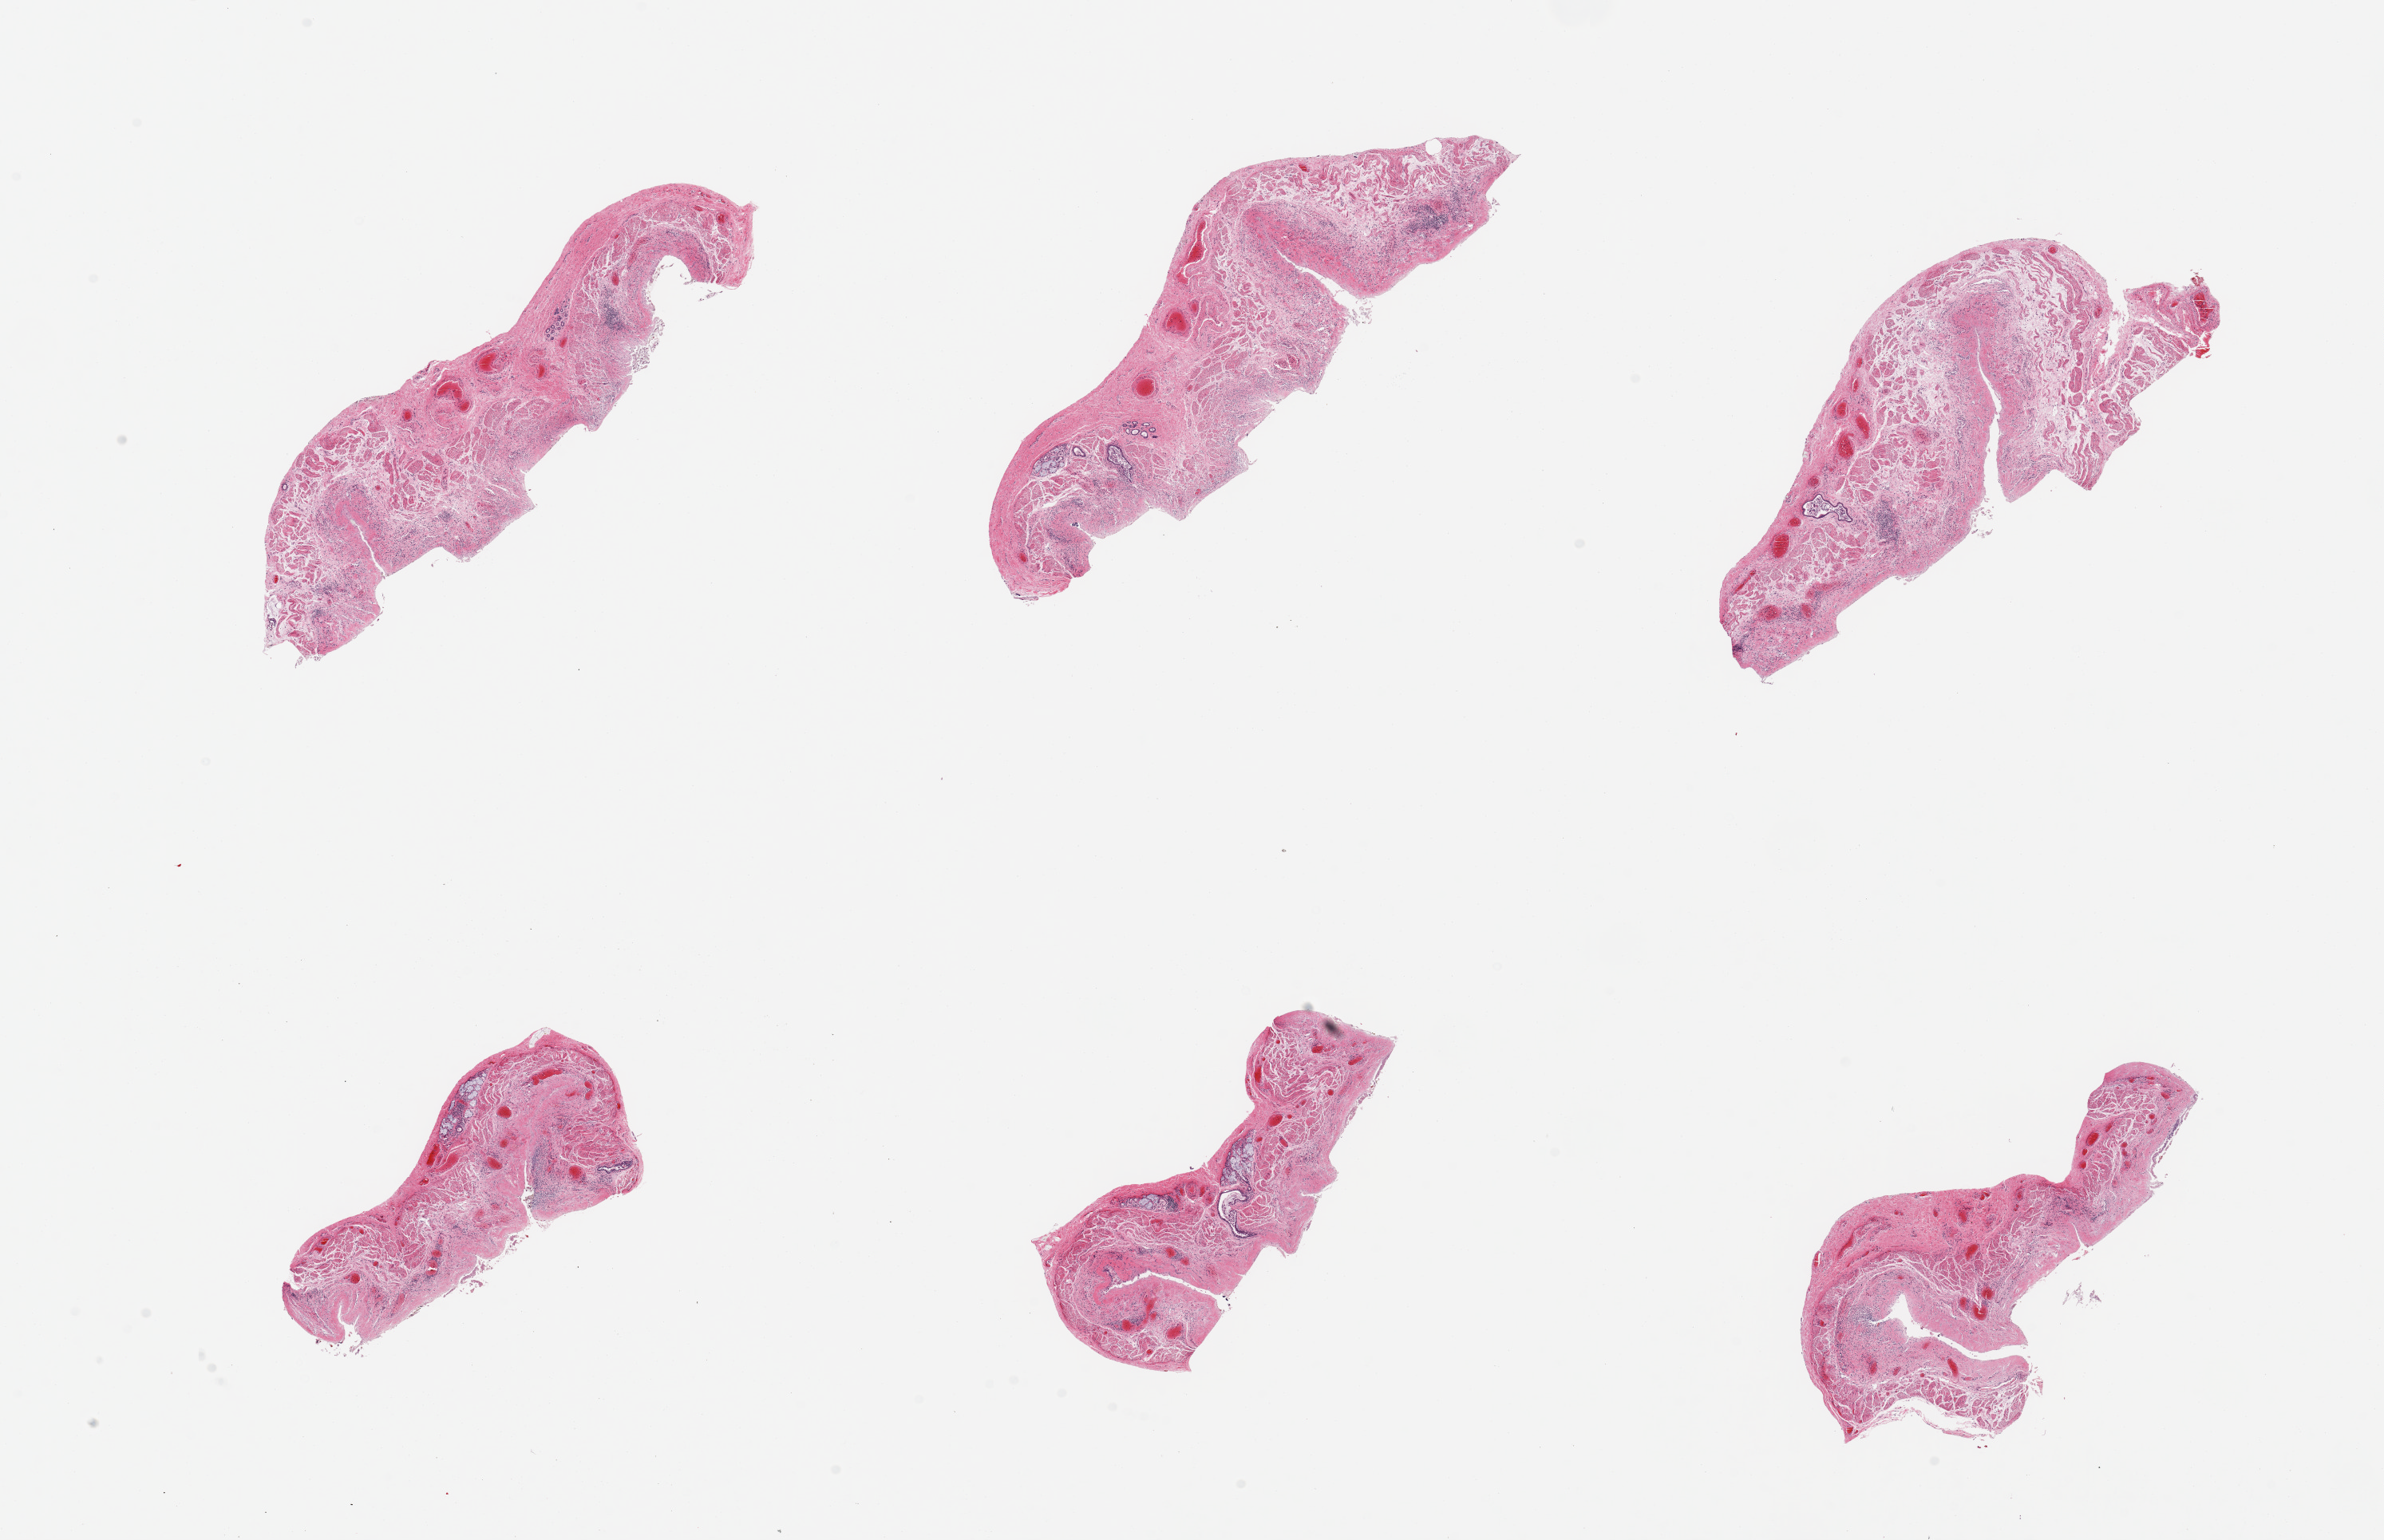
Digitized haematoxylin and eosin-stained section, brightfield — low-resolution overview of the scanned area, about 23.6 x 15.3 mm (from a 20x scan); PAXgene-fixed paraffin-embedded (PFPE) section; sampled site (target tissue): esophageal mucous membrane; tissue donor sample. Male donor.
Review note (as recorded): 6 pieces; completely sloughed epithelium; moderately autolyzed muscularis mucosae and submucosa with mucous glands.